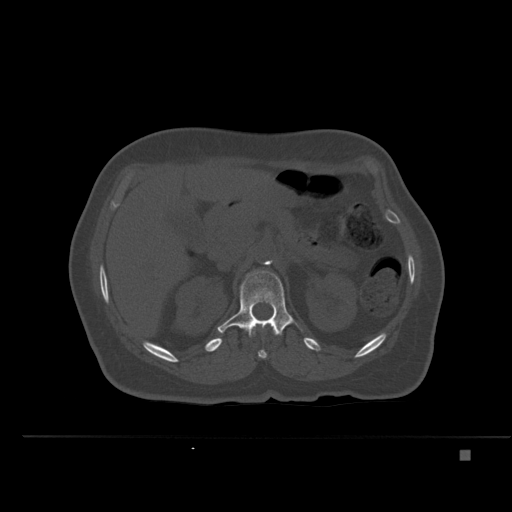
CT including the spine, one axial slice. Position 238 of 477 along the scan axis. Bone window (W 1800 / L 400 HU). 1.5 mm slice thickness. 512 × 512 image matrix, field of view 422 × 422 mm. Female patient, age 74 years. Case-level facts recorded for this patient, not image findings: primary cancer: colon.
Outlined on this slice (semi-automatic segmentation, software-assisted and operator-edited):
- L1 vertebra: bounding box <217,271,294,337> (left, top, right, bottom; pixels)
- T12 vertebra: <251,324,276,359>